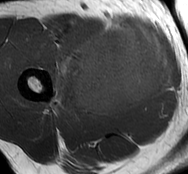
MRI of an extremity soft-tissue mass, one axial slice; MR volume resampled by the dataset authors to the PET/CT grid (not the native acquisition matrix); 188 × 174 image matrix, field of view 184 × 170 mm. Male patient. Case-level facts recorded for this patient, not image findings: histological type: undifferentiated - pleiomorphic; grade: high; site of the primary tumour: right thigh.
Structures marked on this image (expert contour drawn on MRI and transferred to this co-registered scan by the dataset authors):
- gross tumour volume including surrounding oedema: bounding box (x1, y1, x2, y2) in pixels: (52, 24, 171, 116)
- gross tumour volume (mass): (72, 24, 171, 116)